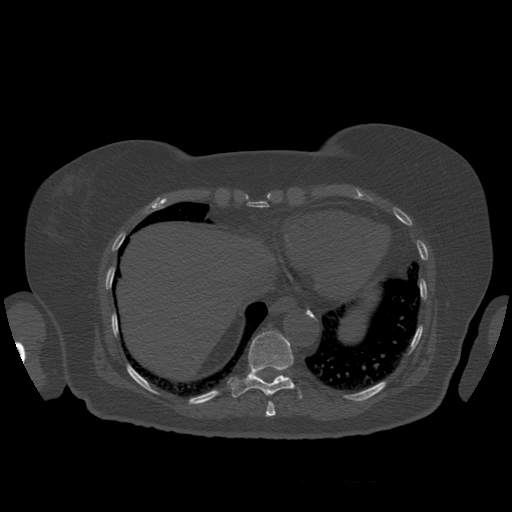
CT including the spine, one axial slice. Slice 341 of 399 in the series (ordered by position). Reconstruction kernel STANDARD. Bone window (W 1800 / L 400 HU). 512 × 512 image matrix, field of view 404 × 404 mm. Patient age 81 years. Case-level facts recorded for this patient, not image findings: primary cancer: renal; vertebrae with lytic lesions (as recorded): L1.
Outlined on this slice (semi-automatic segmentation, software-assisted and operator-edited):
- T10 vertebra: bounding box [x1, y1, x2, y2] px = [232, 331, 302, 399]
- T9 vertebra: [266, 402, 276, 417]